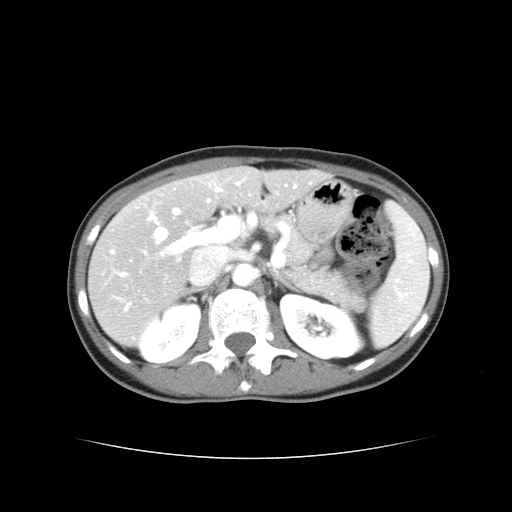
Contrast-enhanced abdominal CT, one axial slice; 120 kVp; soft-tissue window (W 400 / L 40 HU); 512 × 512 image matrix, field of view 340 × 340 mm. Female patient, age 54 years. Case-level facts recorded for this patient, not image findings: diagnosis: colorectal cancer liver metastases, imaged before liver resection; multiple liver metastases: yes; largest metastasis: 1.1 cm; disease in both lobes: yes.
Annotated regions visible in this slice (expert manual segmentation):
- hepatic veins: box from (x=121, y=186) to (x=296, y=277) px
- liver: (x=90, y=168)–(x=325, y=341)
- planned liver remnant (the part of the liver to remain after resection): (x=216, y=168)–(x=325, y=209)
- portal vein (with intrahepatic branches): (x=149, y=183)–(x=239, y=256)